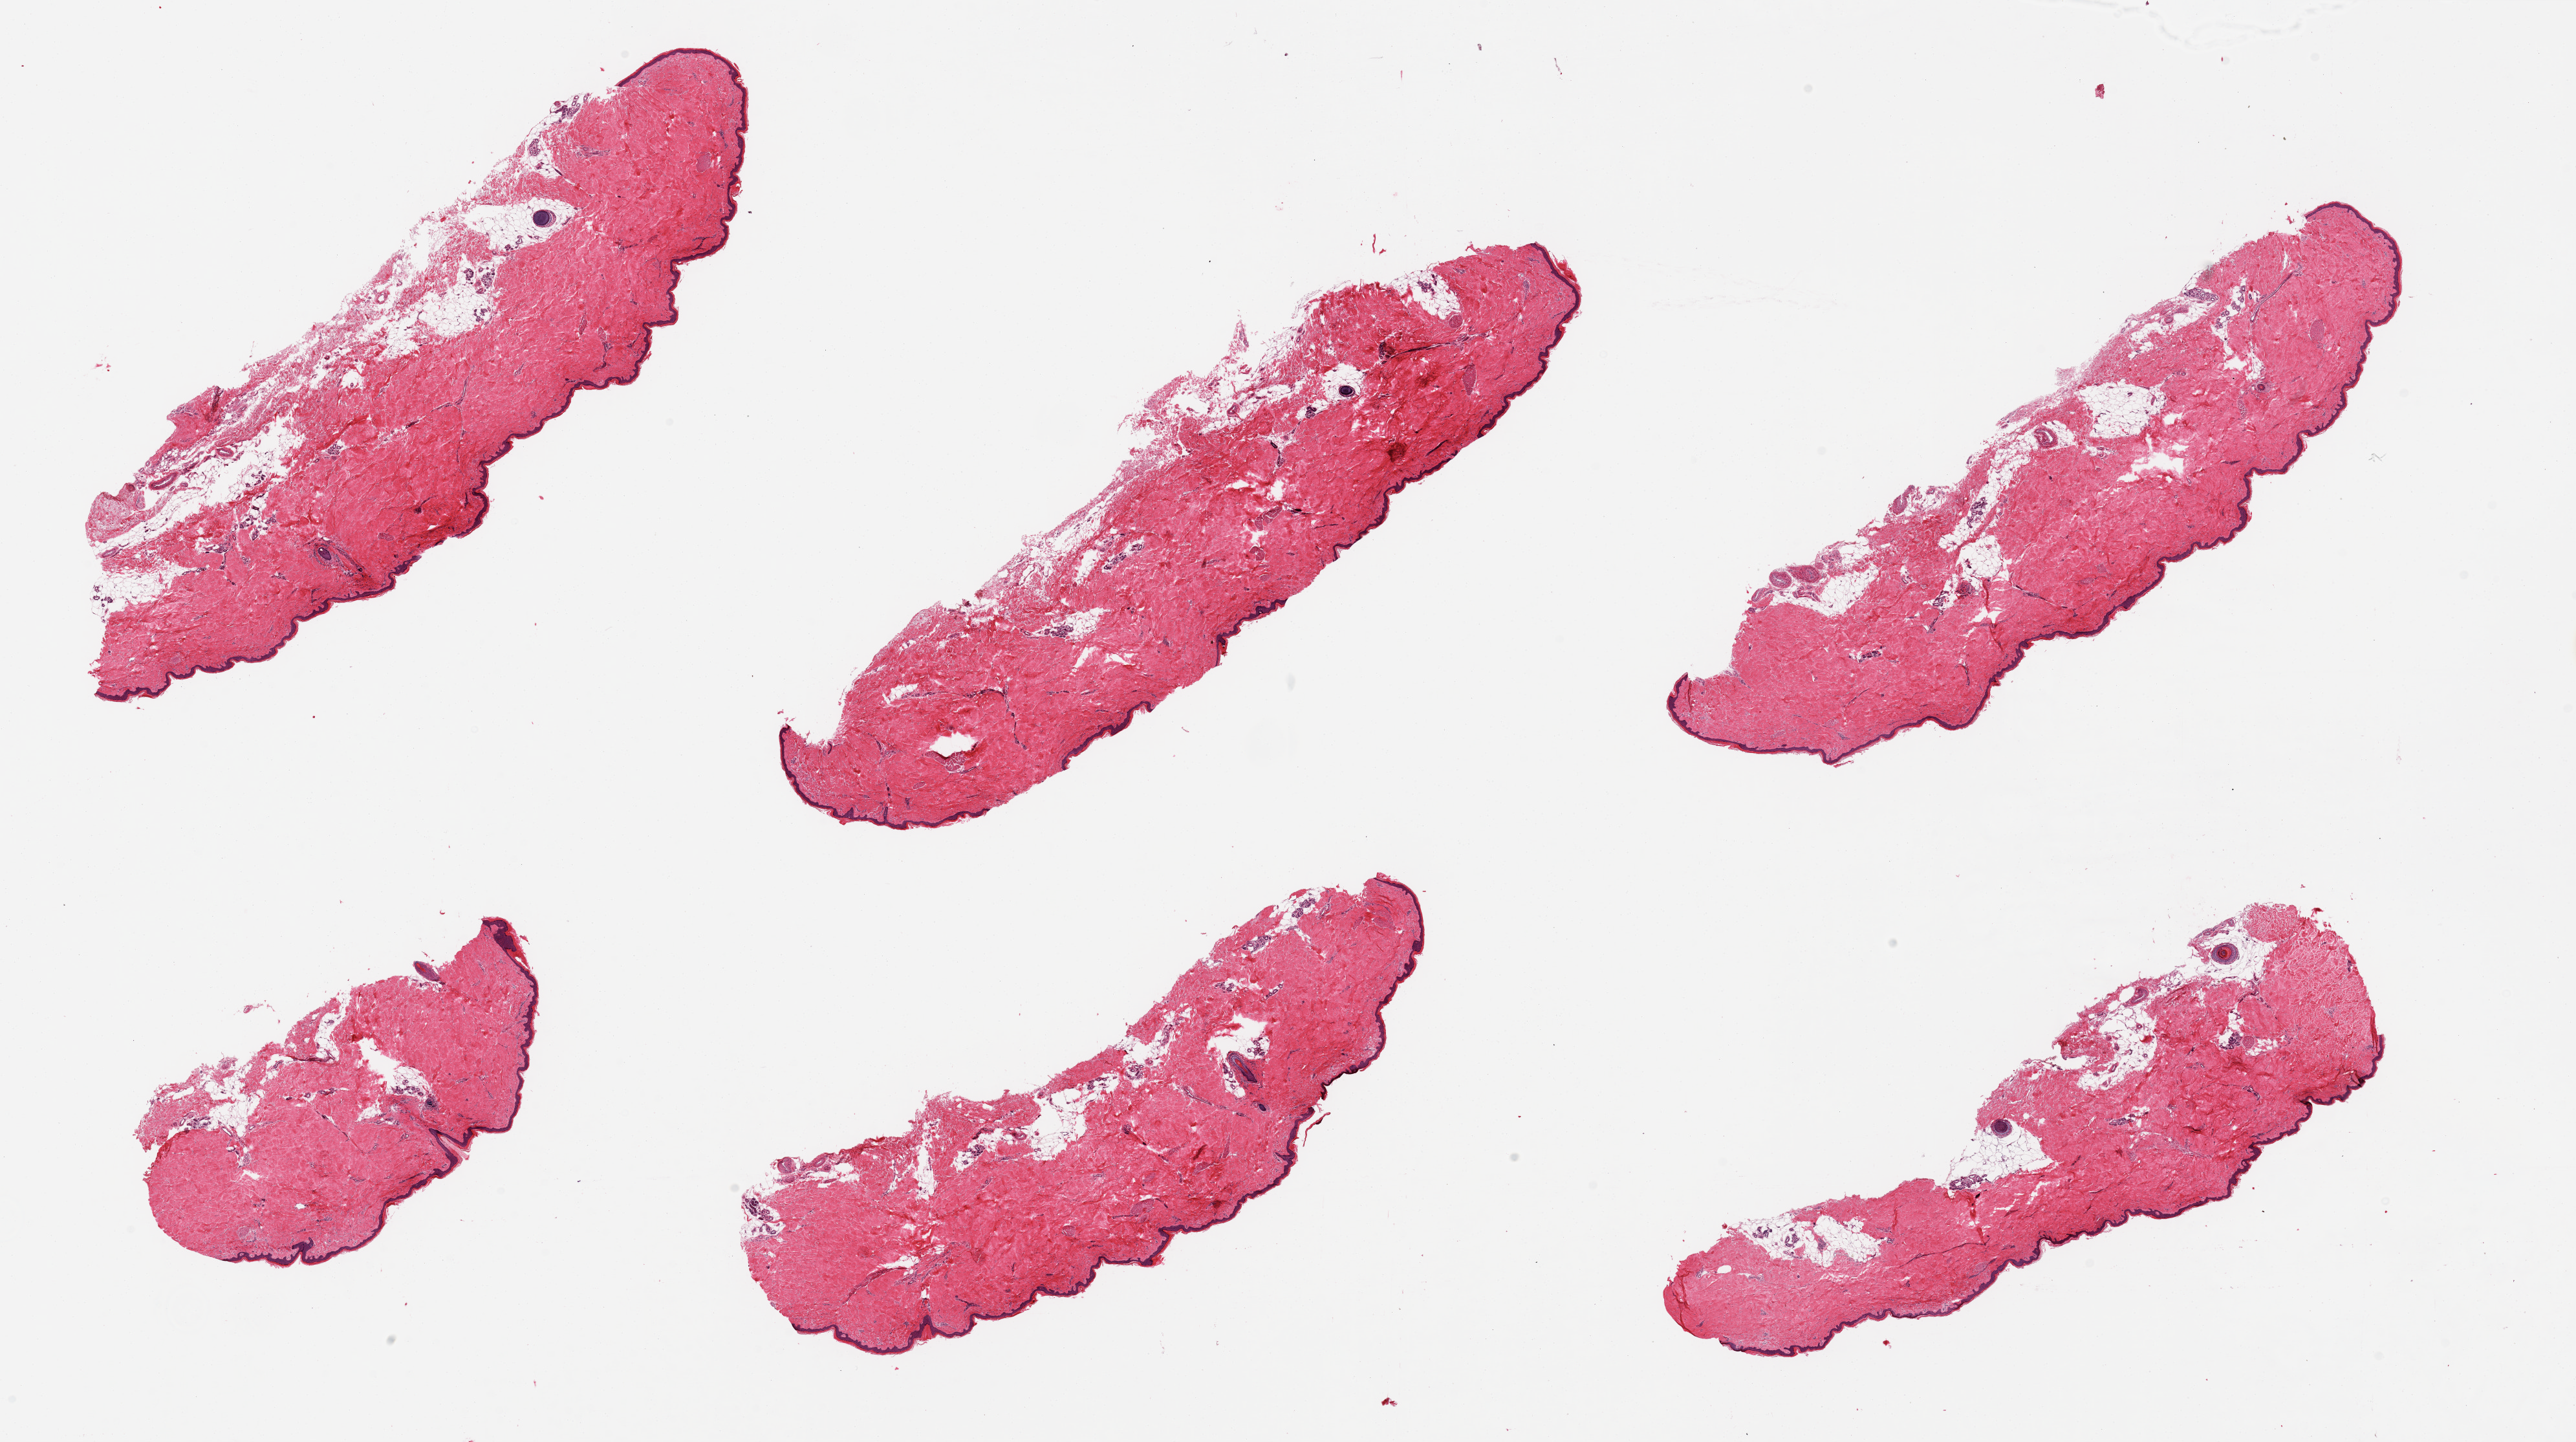
Whole-slide image, haematoxylin and eosin stain — low-resolution overview of the scanned area, about 31.5 x 17.6 mm (from a 20x scan), PAXgene-fixed paraffin-embedded (PFPE) section, sampled site (target tissue): skin of lower leg, donor tissue sample. Donor sex: female.
• reviewer comment on this tissue sample: 6 pieces, trace dermal fat; squamous epithelium is ~40 microns